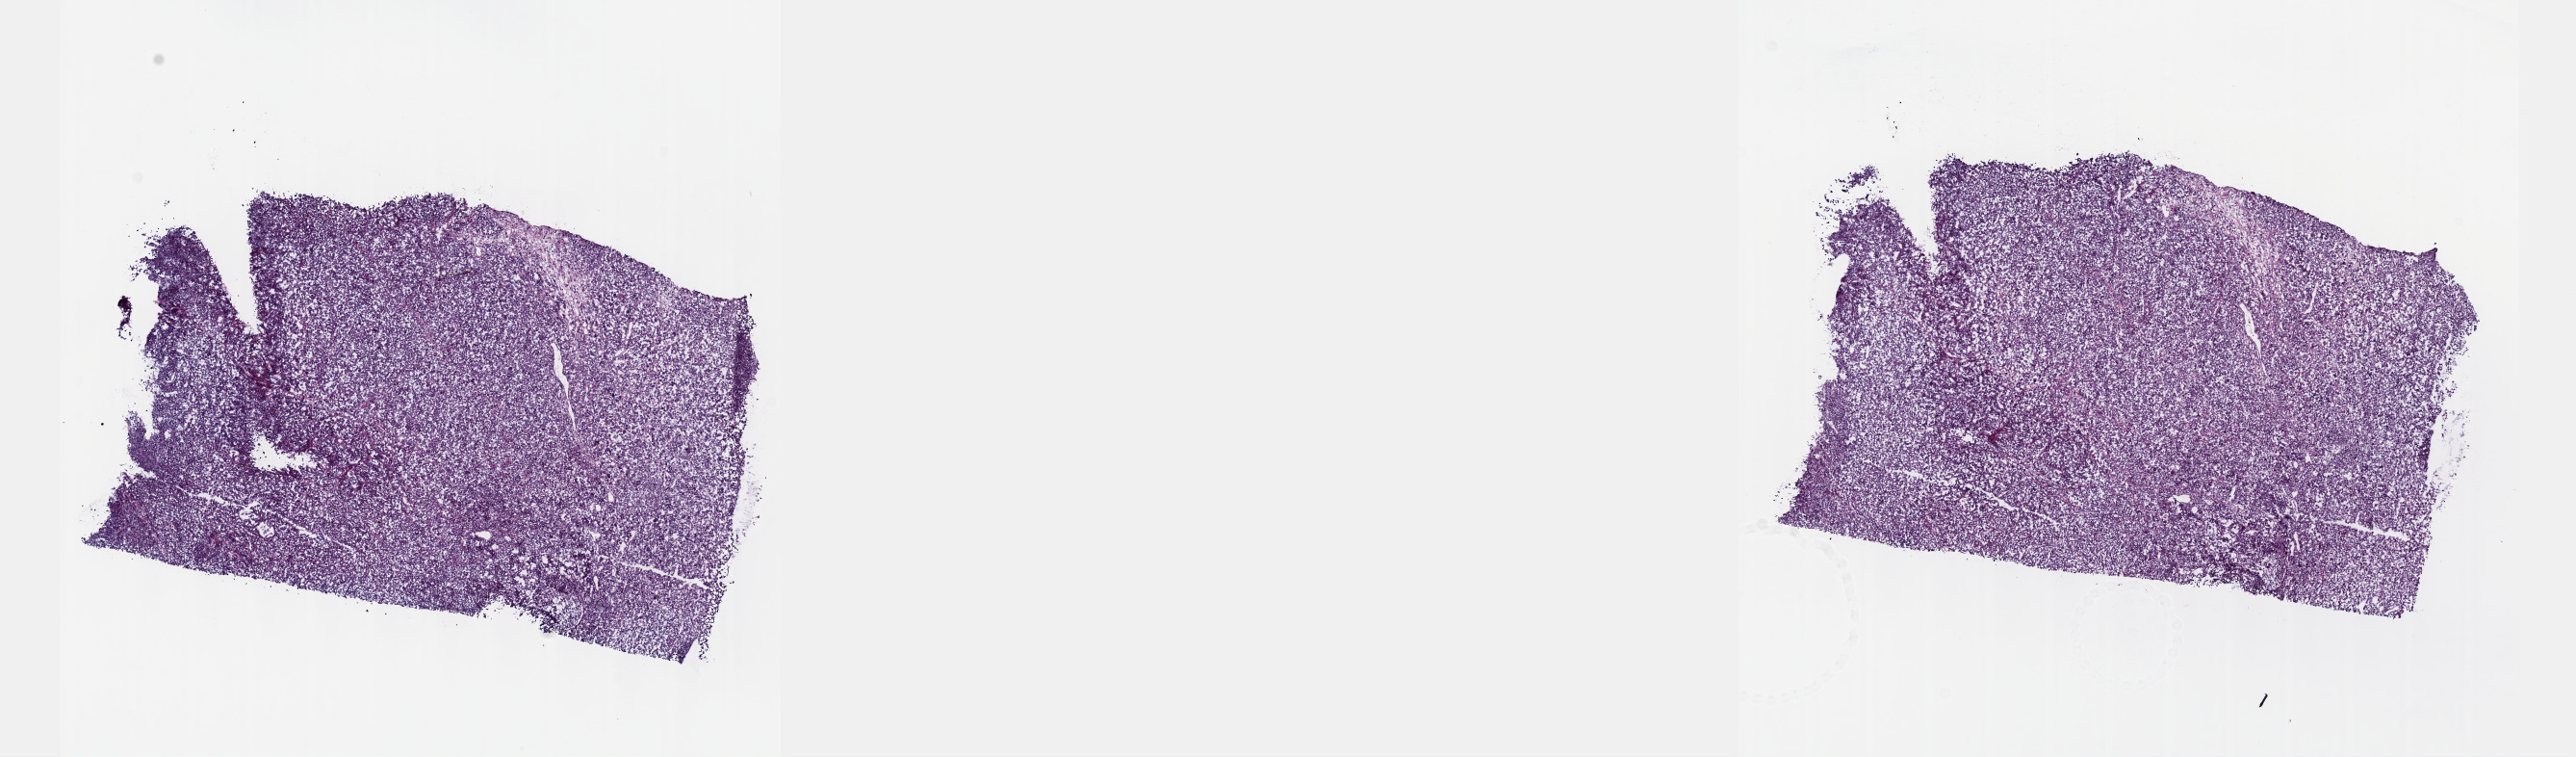
Whole-slide histology image, Hematoxylin and eosin (H&E) stained — whole scanned area (about 21.6 x 6.4 mm) shown as a low-resolution overview, frozen section, metastatic tumour sample, sampled site: connective, subcutaneous and other soft tissues of trunk. Male patient; age at initial diagnosis 87 years. Pathologist review of this section (percent, as recorded): tumour cells 100%, tumour nuclei 80%, normal cells 0%, stromal cells 0%, necrosis 0%. Inflammatory infiltration, as recorded: lymphocyte infiltration 3%, monocyte infiltration 0%, neutrophil infiltration 0%.
This section: metastatic tumour tissue. Patient diagnosis: Malignant melanoma, NOS.